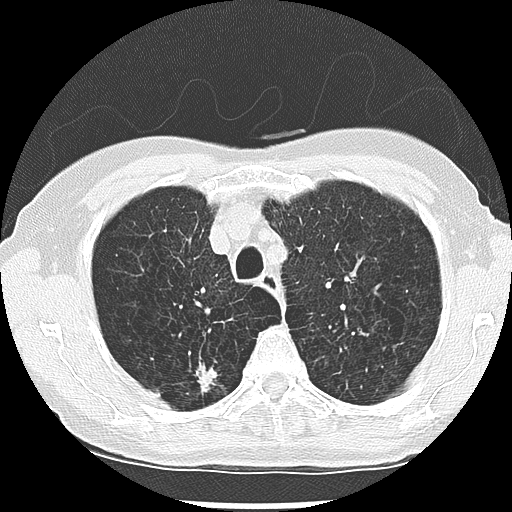
Low-dose screening chest CT, one axial slice. Slice 215 of 265 in the series (ordered by position). Reconstruction kernel LUNG. Lung window (W 1500 / L -600 HU). 512 × 512 image matrix, field of view 300 × 300 mm.
Structures marked on this image (manually delineated by an expert):
- lesion 1 (nodule, upper lobe of right lung): bounding box (x1, y1, x2, y2) in pixels: (196, 365, 217, 393)